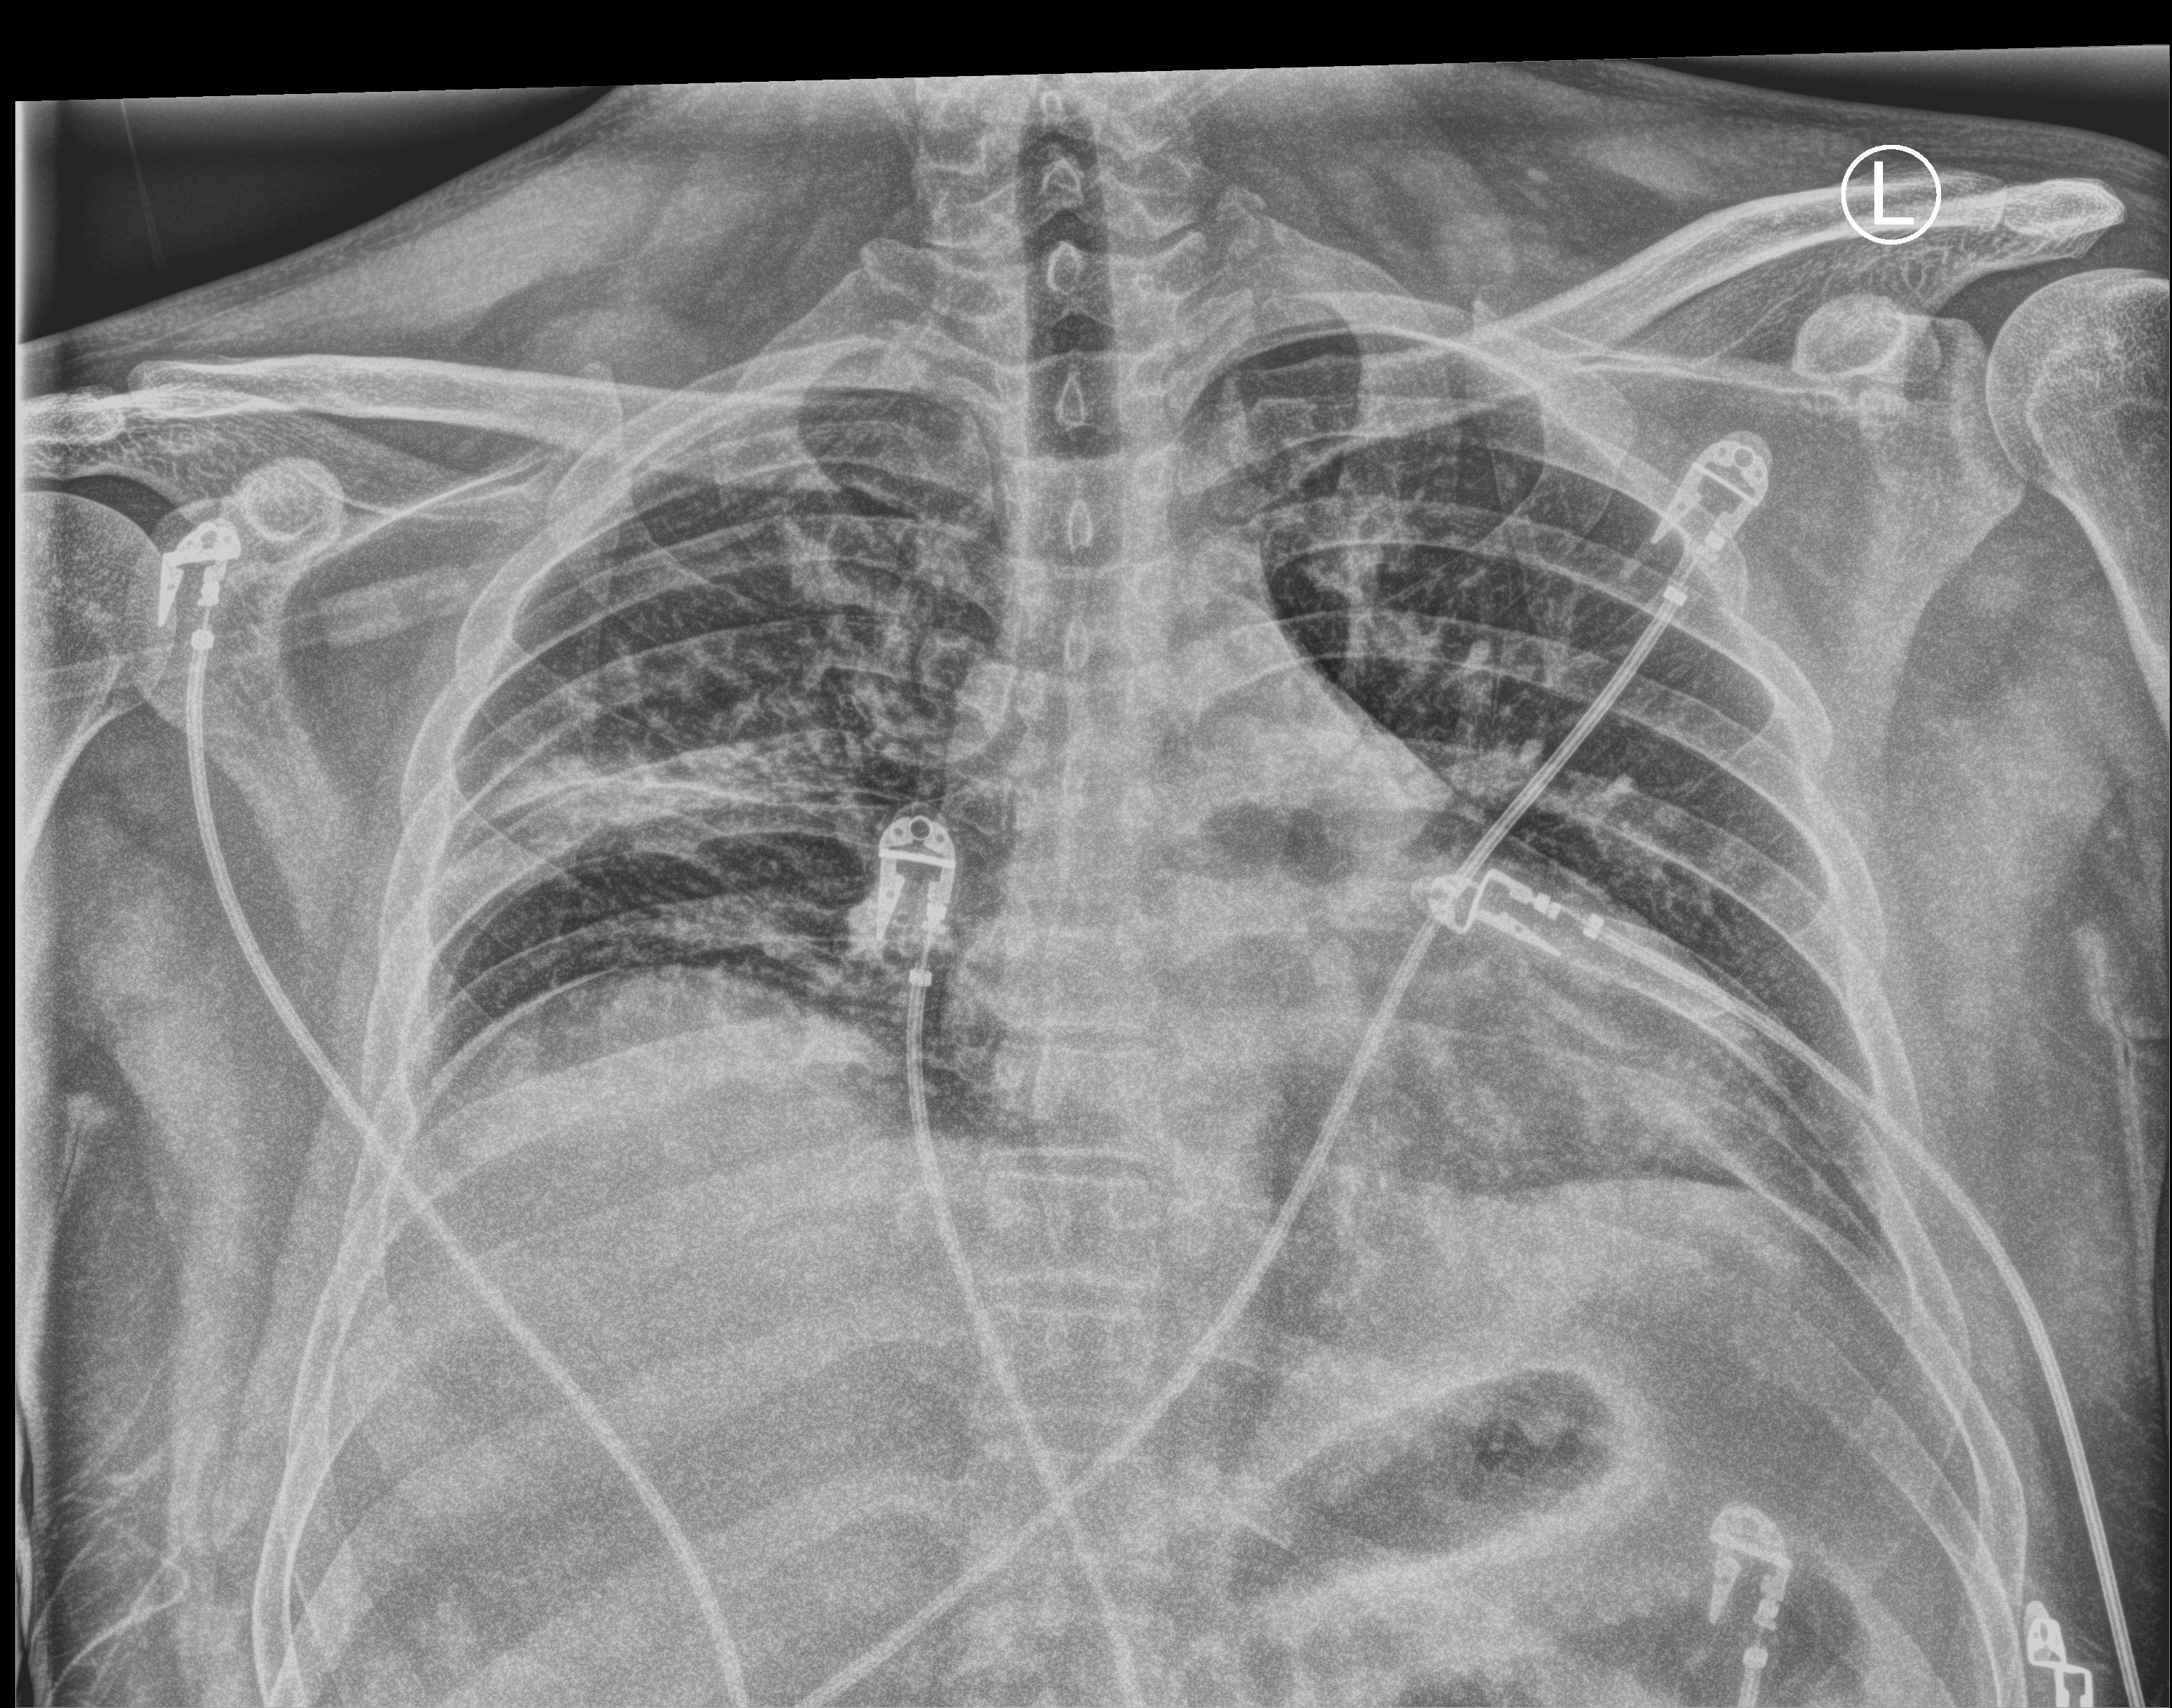
Chest X-ray (portable), anteroposterior (AP) projection. Adult patient hospitalised with COVID-19, age 18–59 years.
Admission-level facts for this patient (not findings on this image; timing relative to this image not recorded):
- other chronic lung disease (admission record): no
- COPD (admission record): no